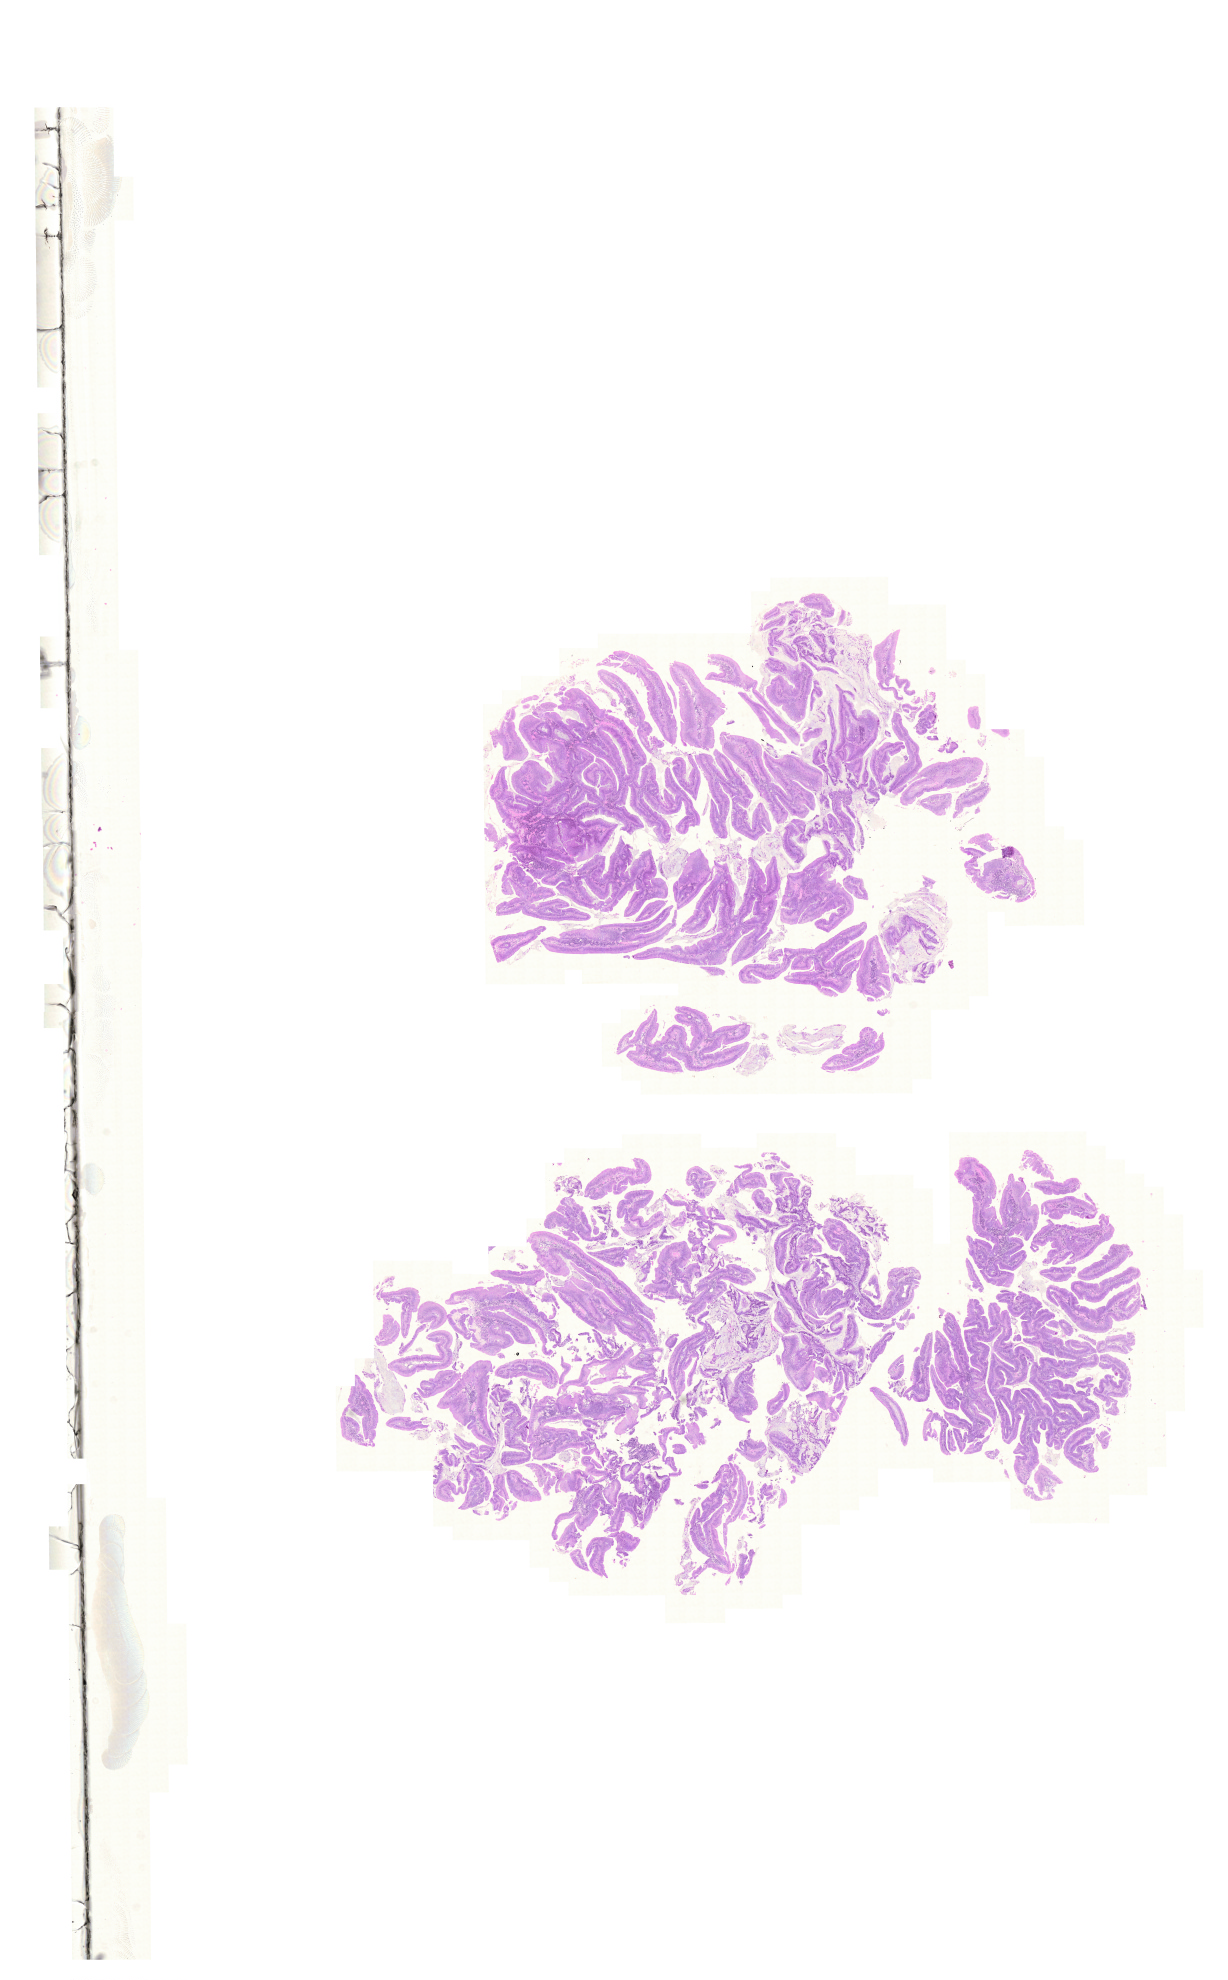
Whole-slide histology image, H&E-stained, a low-resolution overview of the entire scanned area, about 18.3 x 29.5 mm (from a 20x scan), formalin-fixed paraffin-embedded (FFPE) diagnostic section, colon, primary tumour sample. Male patient; age at initial diagnosis 81 years.
* AJCC pathologic stage: II (5th edition)
* lymph nodes positive (case pathology): 0 of 14 examined
* TNM: T3 N0 M0
* histologic diagnosis: Adenocarcinoma, NOS (descending colon)